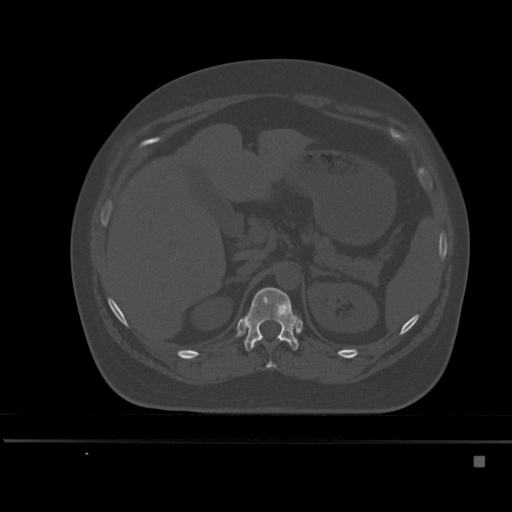
CT including the spine, one axial slice; position 218 of 495 along the scan axis; bone window (W 1800 / L 400 HU); 1.5 mm slice thickness; 512 × 512 image matrix, field of view 404 × 404 mm. Female patient, age 33 years. Case-level facts recorded for this patient, not image findings: primary cancer: breast; vertebrae with lytic lesions (as recorded): T1.
Structures marked on this image (semi-automatic segmentation, software-assisted and operator-edited):
- T11 vertebra: box from (x=266, y=361) to (x=276, y=369) px
- T12 vertebra: (x=244, y=287)–(x=299, y=351)